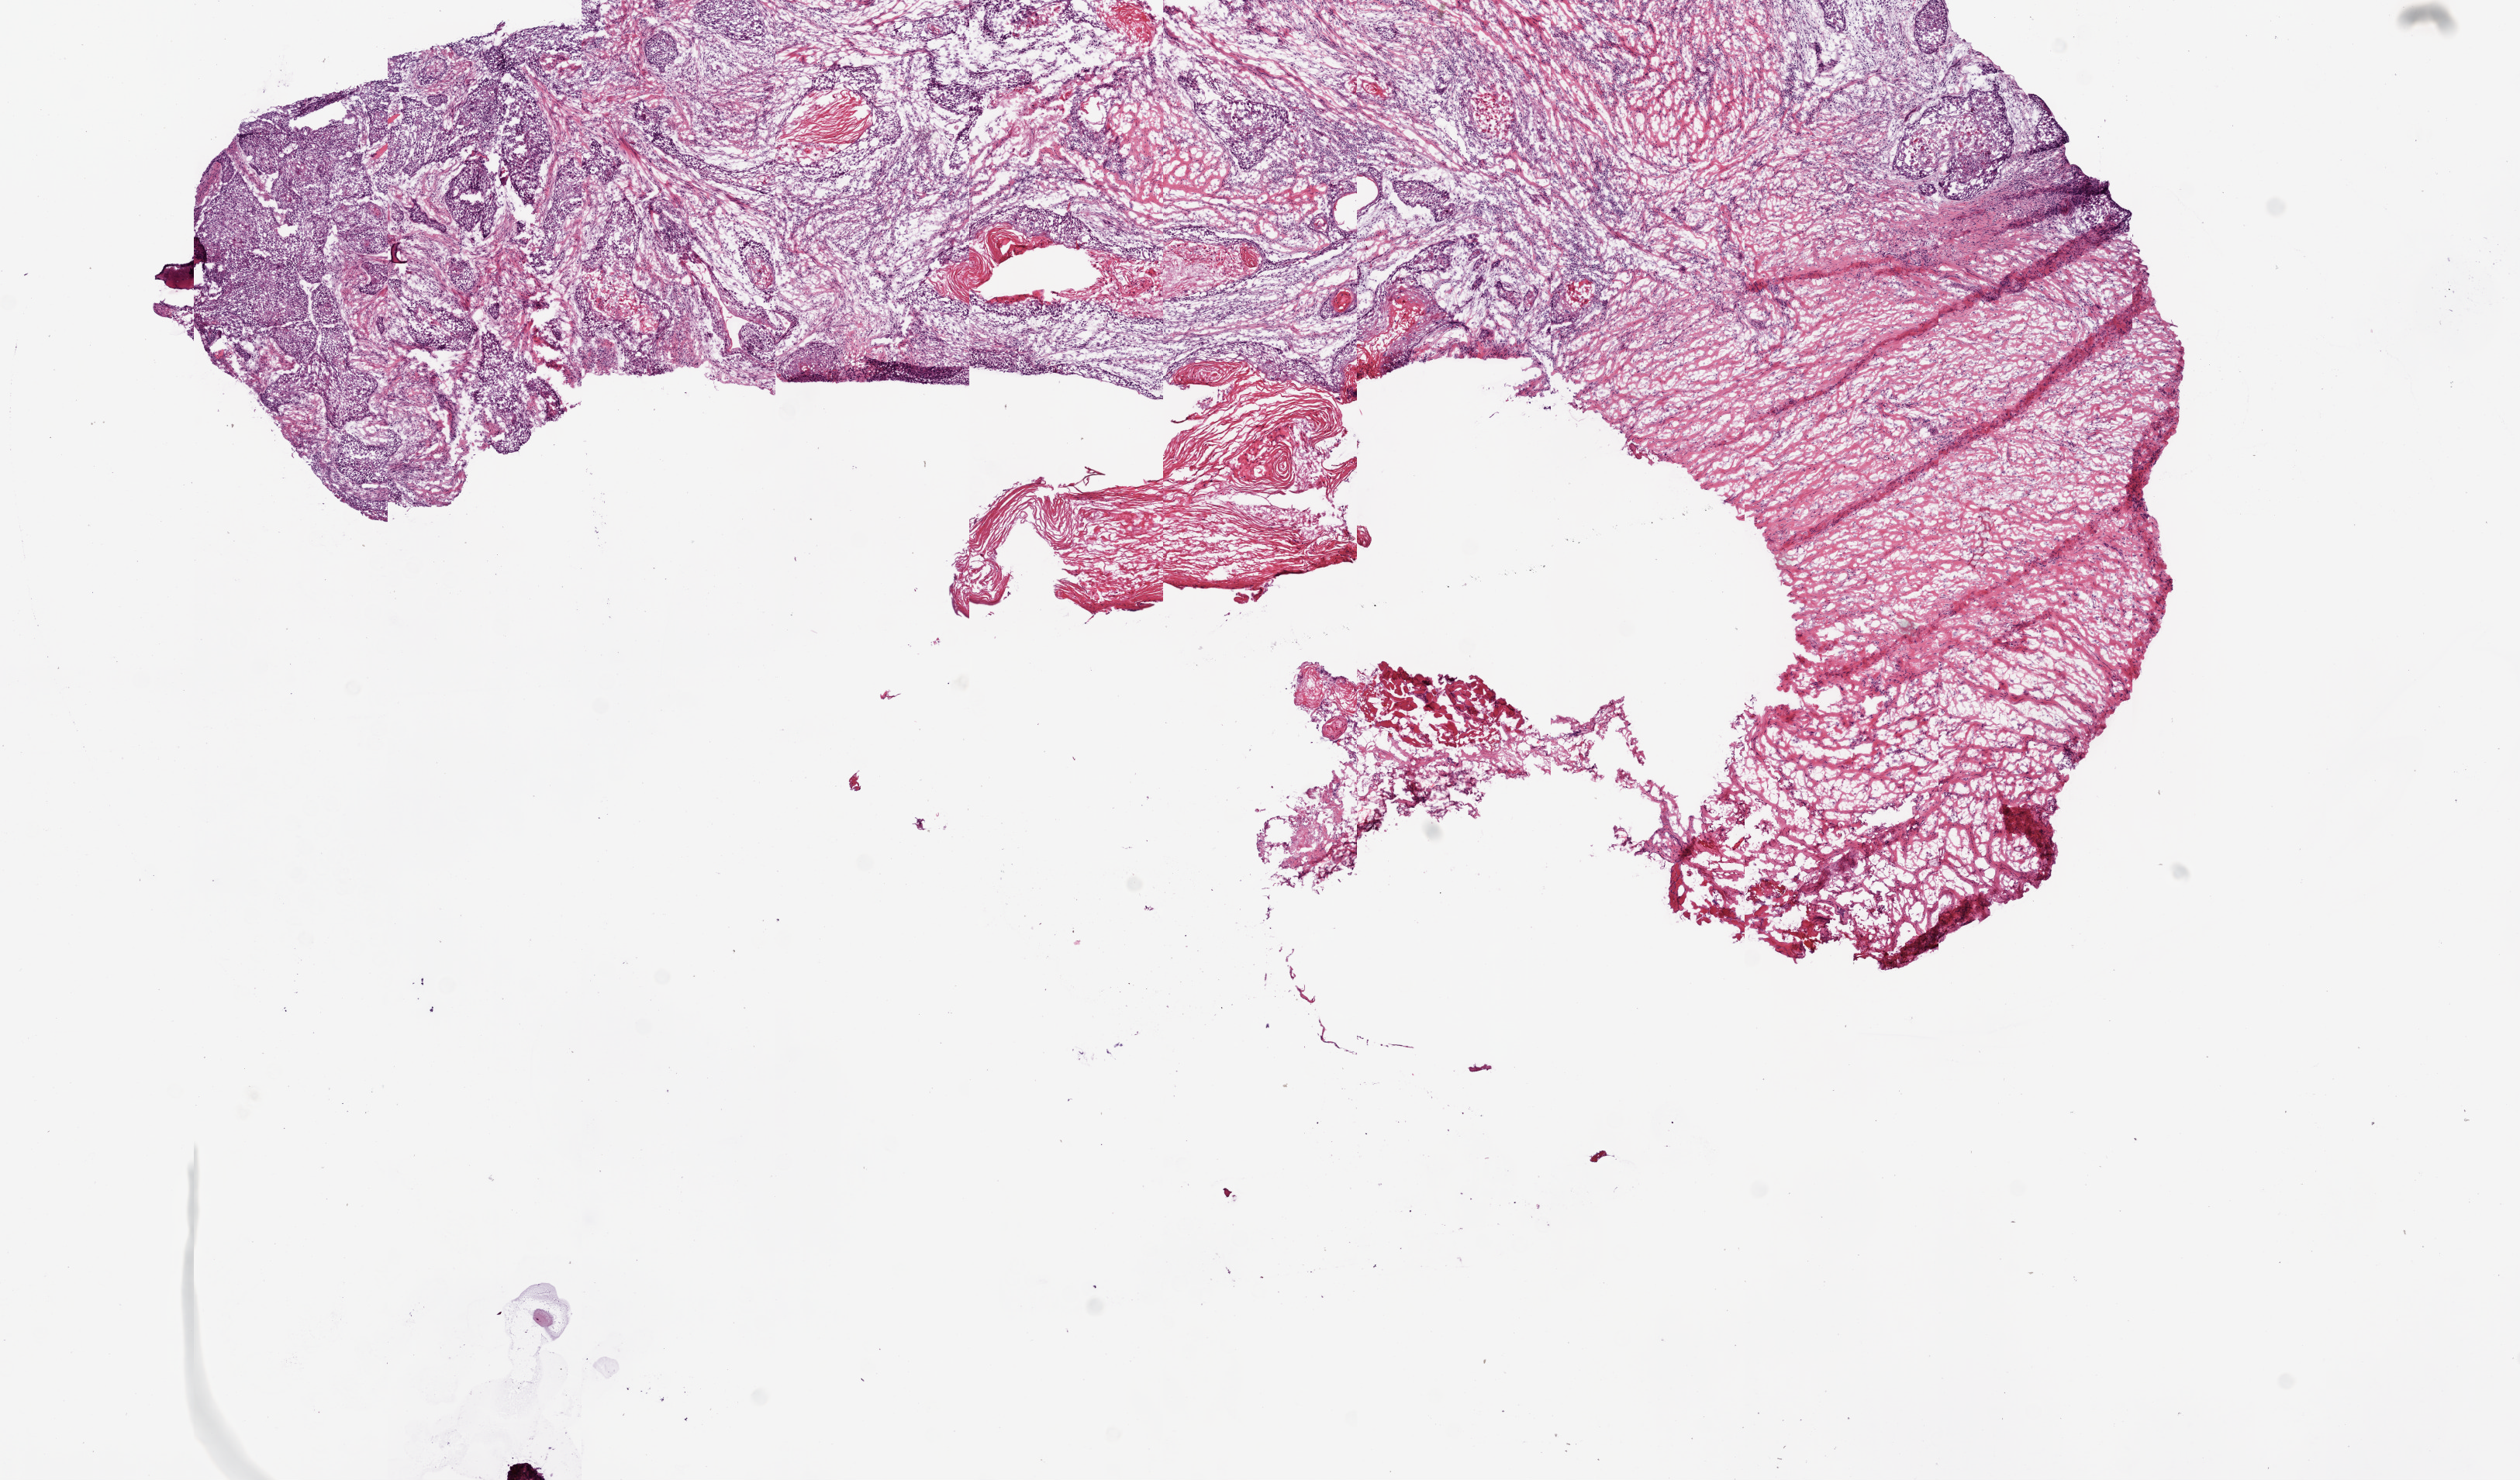
Whole-slide histology image, H&E-stained, shown as a low-resolution overview of the whole scanned area (about 13.0 x 7.7 mm, acquisition: 20x scan), frozen section from the bottom of the tissue portion, sample: primary tumour, head and neck. Female, age 79 years at initial diagnosis. Histologic grade: G2 (moderately differentiated). Composition of this section per pathologist review: tumour cells 48%, tumour nuclei 70%, normal cells 0%, stromal cells 50%, necrosis 2%.
Histologic diagnosis: Squamous cell carcinoma, NOS (mouth, NOS). Lymph nodes positive (case pathology): 0 of 26 examined. AJCC pathologic stage: IVA (6th edition).